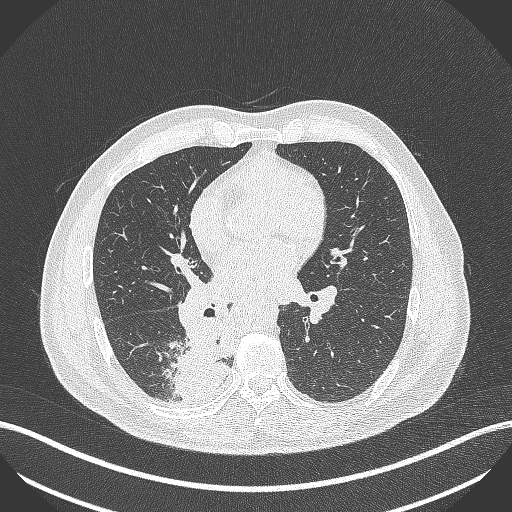
Chest CT, one axial slice; slice 229 of 451 in the series (ordered by position); reconstruction kernel B70f; 100 kVp; lung window (W 1500 / L -600 HU); 1 mm slice thickness; 512 × 512 image matrix, field of view 400 × 400 mm. Male patient, age 61 years. From the clinical record (not read from this slice): clinical TNM (as recorded): T1 N0 M0; histopathological grade: G3.
Annotated regions visible in this slice (rectangle marked by the reading radiologist):
- lung tumour (recorded histology: small cell carcinoma): bounding box [x1, y1, x2, y2] px = [173, 311, 234, 402]